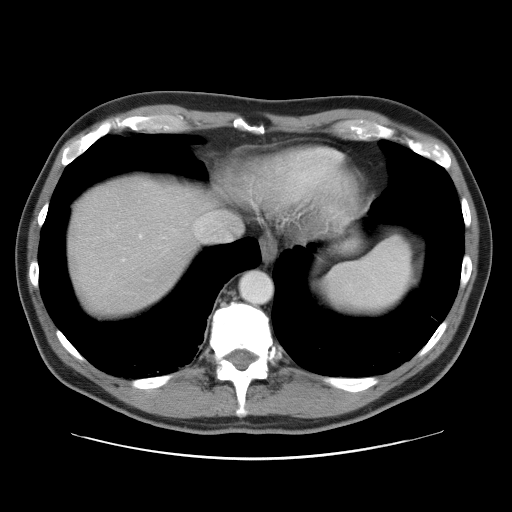
Contrast-enhanced abdominal CT, one axial slice; slice 47 of 52 in the series (ordered by position); soft-tissue window (W 400 / L 40 HU); 5 mm slice thickness; 512 × 512 image matrix. Male patient, age 70 years. Case-level facts recorded for this patient, not image findings: diagnosis: colorectal cancer liver metastases, imaged before liver resection; multiple liver metastases: yes.
Annotated regions visible in this slice (expert manual segmentation):
- hepatic veins: box from (x=195, y=212) to (x=219, y=239) px
- liver: (x=66, y=176)–(x=215, y=318)
- planned liver remnant (the part of the liver to remain after resection): (x=179, y=182)–(x=212, y=199)